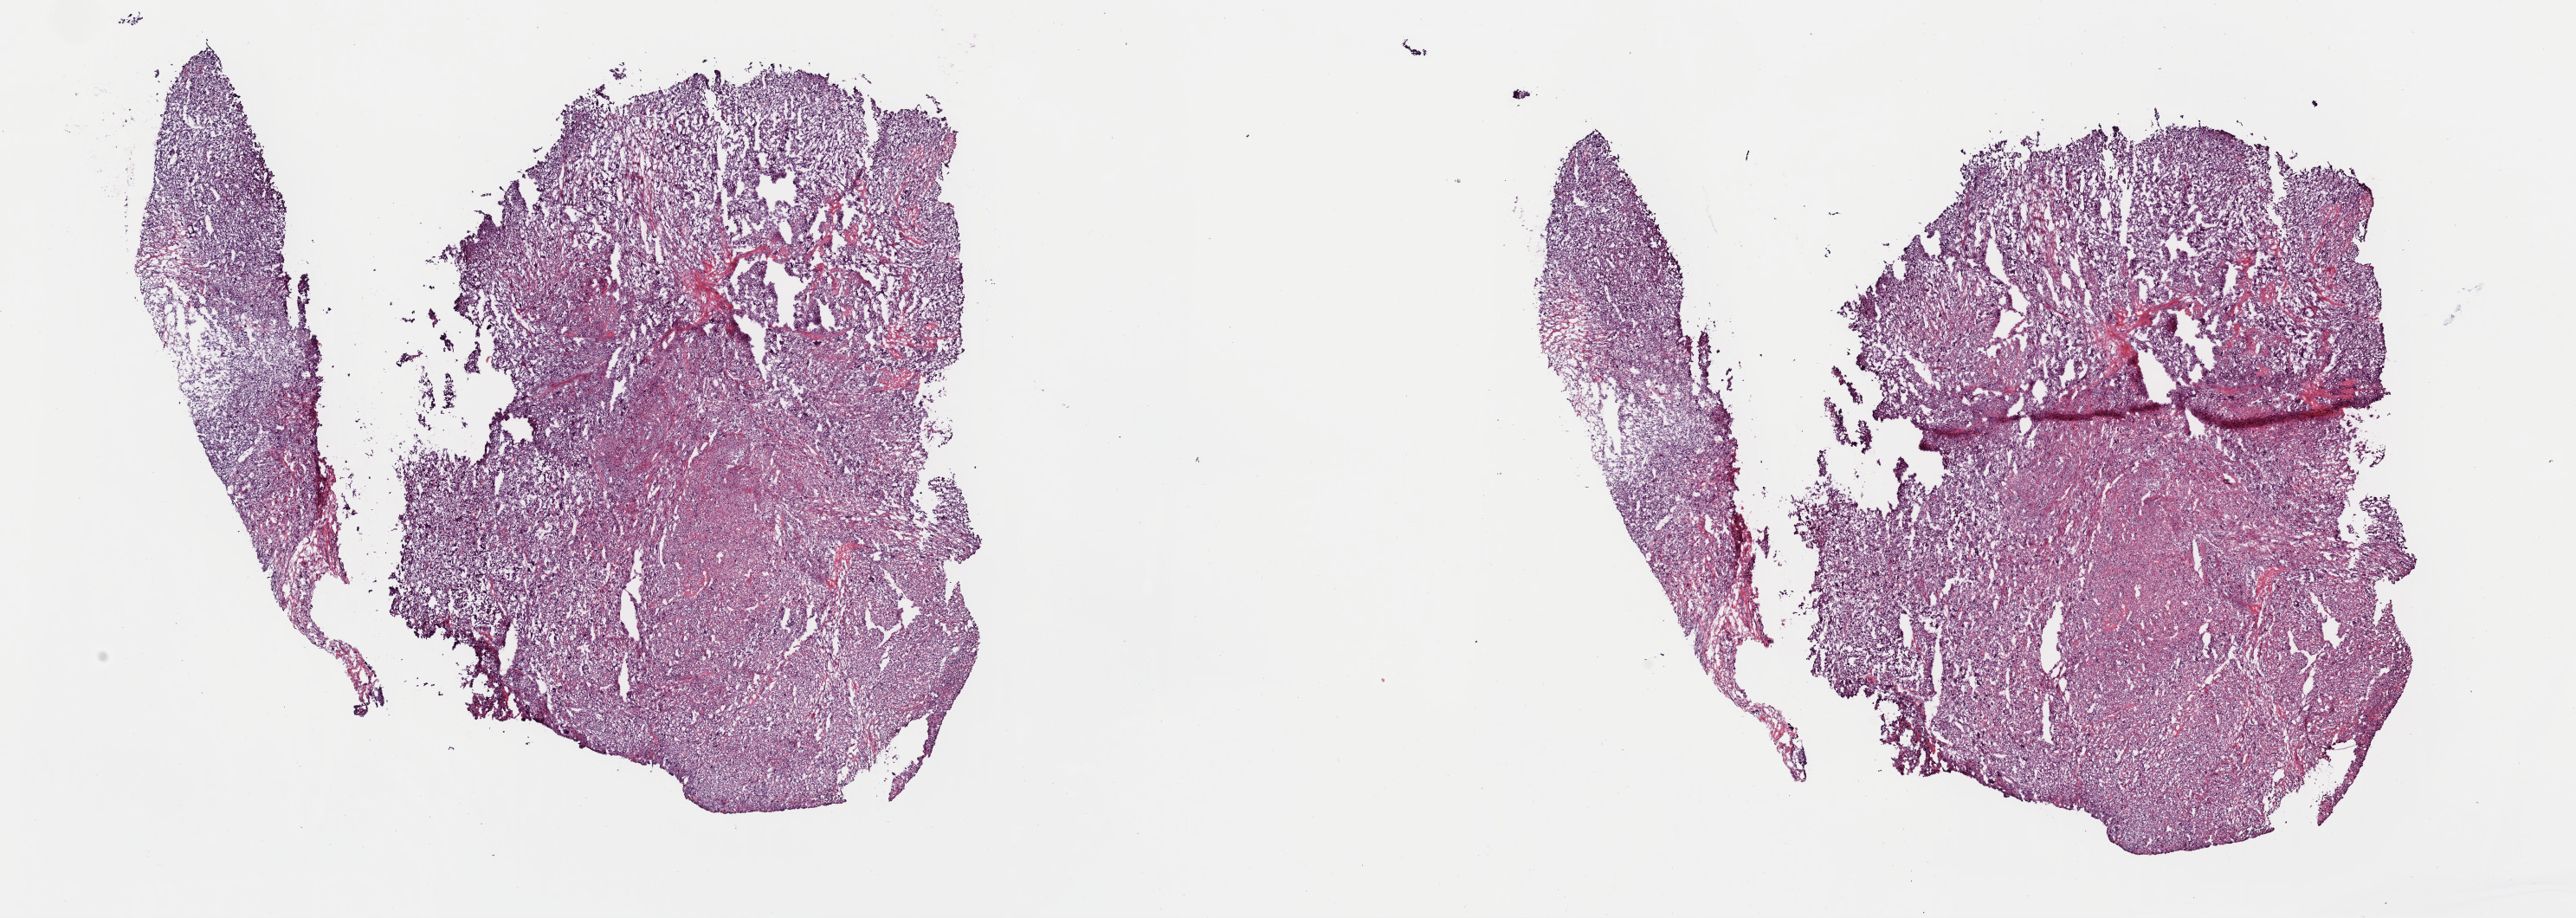
Hematoxylin and eosin (H&E) stained whole-slide image, a low-resolution overview of the entire scanned area, about 23.5 x 8.4 mm. Frozen section from the top of the tissue portion. Sample: primary tumour, connective, subcutaneous and other soft tissues. Female, age 60 years at initial diagnosis. Slide review estimates, as recorded: tumour cells 85%, tumour nuclei 100%, normal cells 0%, stromal cells 15%, necrosis 0%. Infiltration values recorded for this section: lymphocyte infiltration 2%, monocyte infiltration 1%, neutrophil infiltration 0%.
Histologic diagnosis: Undifferentiated sarcoma (connective, subcutaneous and other soft tissues of lower limb and hip).